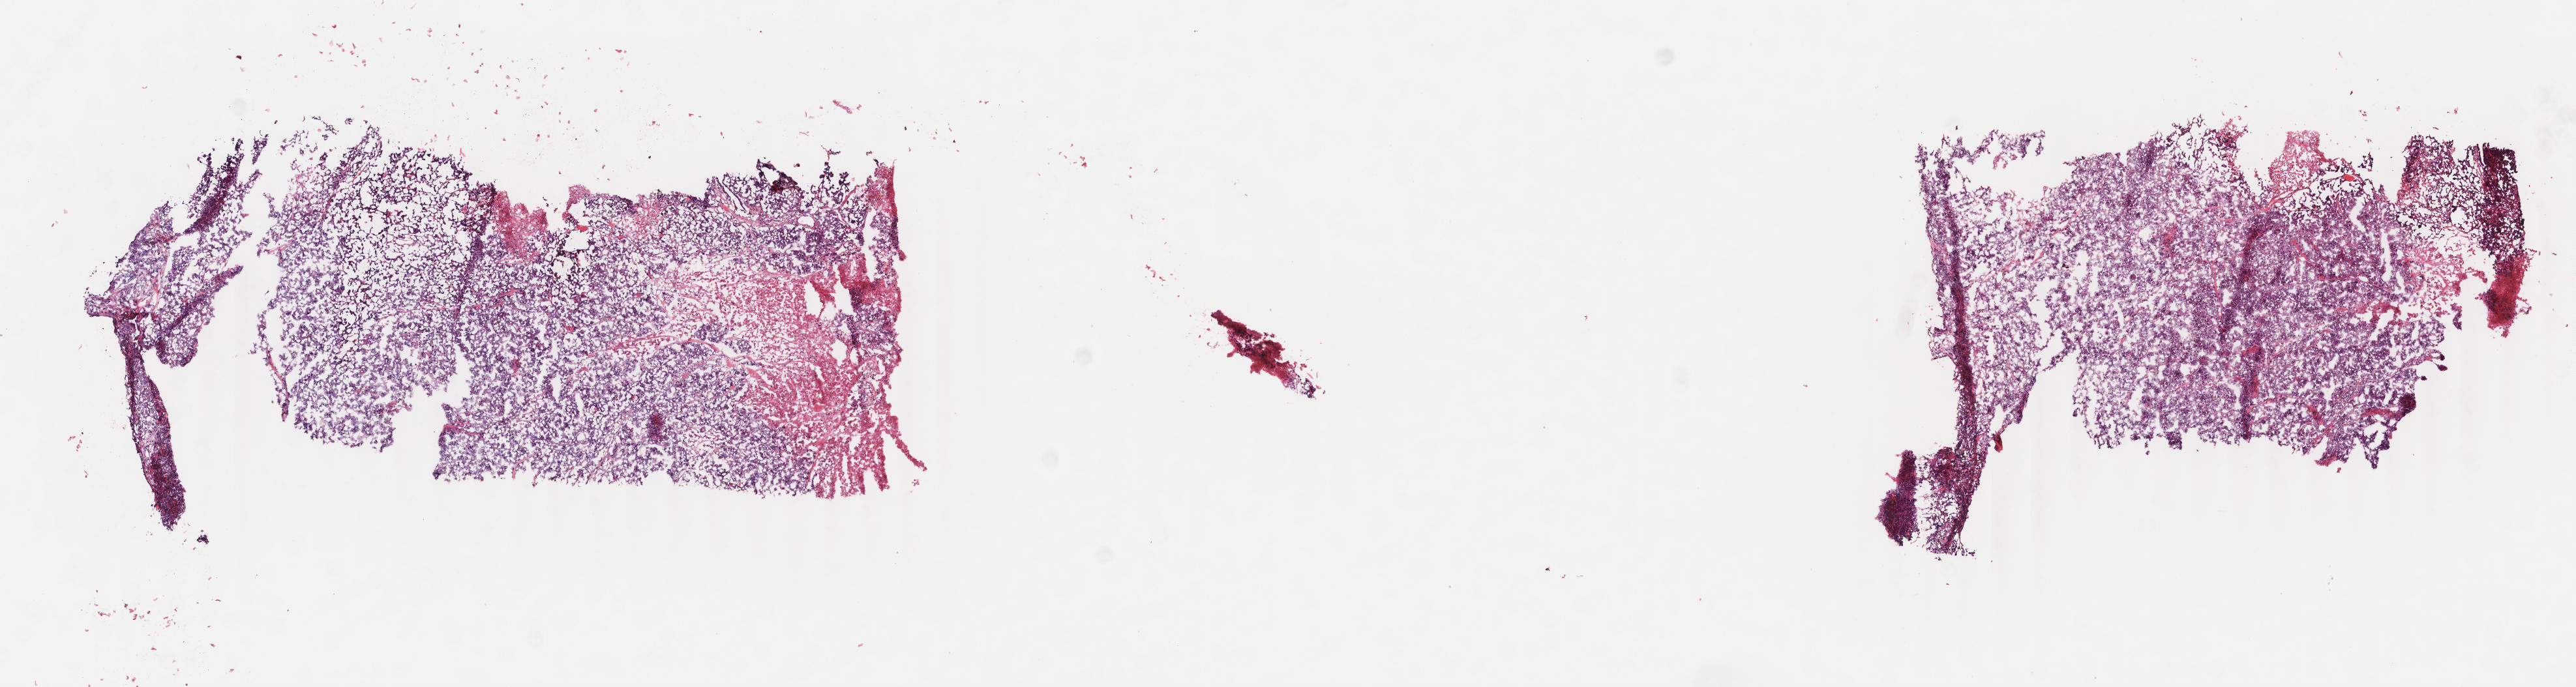
Whole-slide histology image, H&E — whole scanned area (about 15.7 x 4.2 mm) shown as a low-resolution overview; frozen section; primary tumour sample from the breast. Female patient; age at initial diagnosis 48 years. Slide review estimates, as recorded: tumour cells 80%, tumour nuclei 80%, normal cells 0%, stromal cells 0%, necrosis 20%. Infiltration values recorded for this section: lymphocyte infiltration 10%, monocyte infiltration 0%, neutrophil infiltration 0%.
Laterality: left. Lymph nodes positive (case pathology): 16 of 21 examined. Pathologic diagnosis: Infiltrating duct carcinoma, NOS.